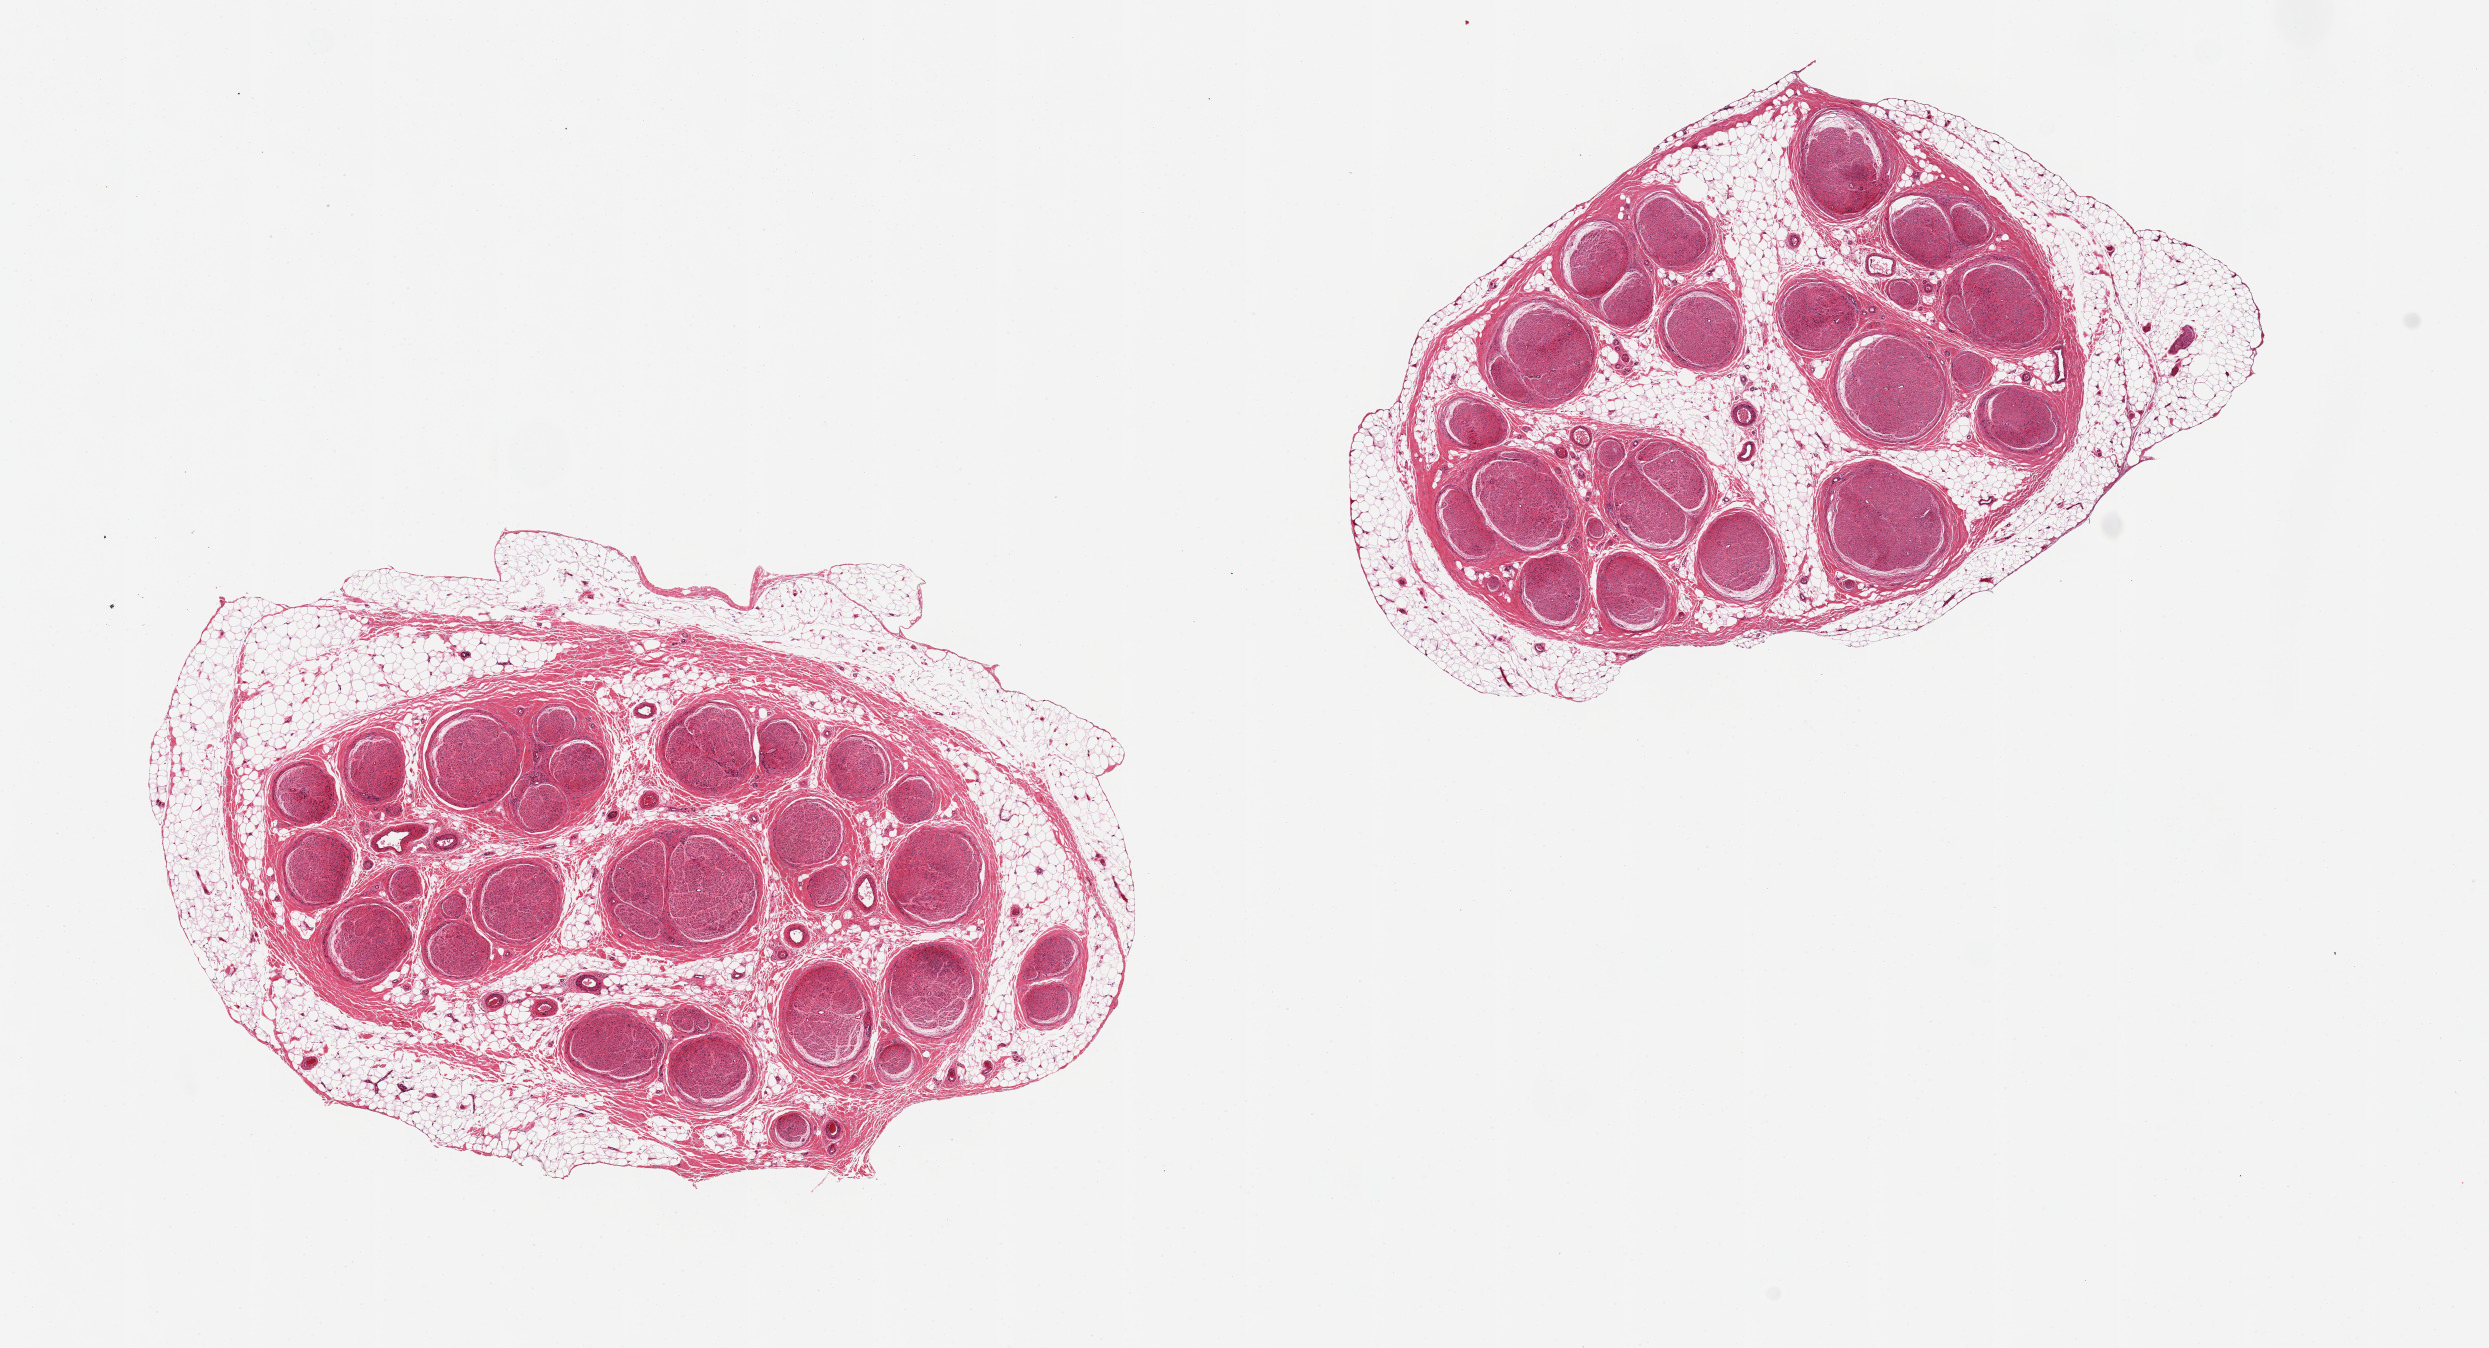
Whole-slide image, hematoxylin and eosin (H&E) stain, brightfield — whole scanned area (about 19.7 x 10.7 mm, acquisition: 20x scan) shown as a low-resolution overview, PAXgene-fixed, paraffin-embedded tissue, target tissue: tibial nerve, donor tissue sample.
Pathologist's review note for this sample: 2 ~6x4mm aliquots, both with ~0.5mm rim of adherent fat.